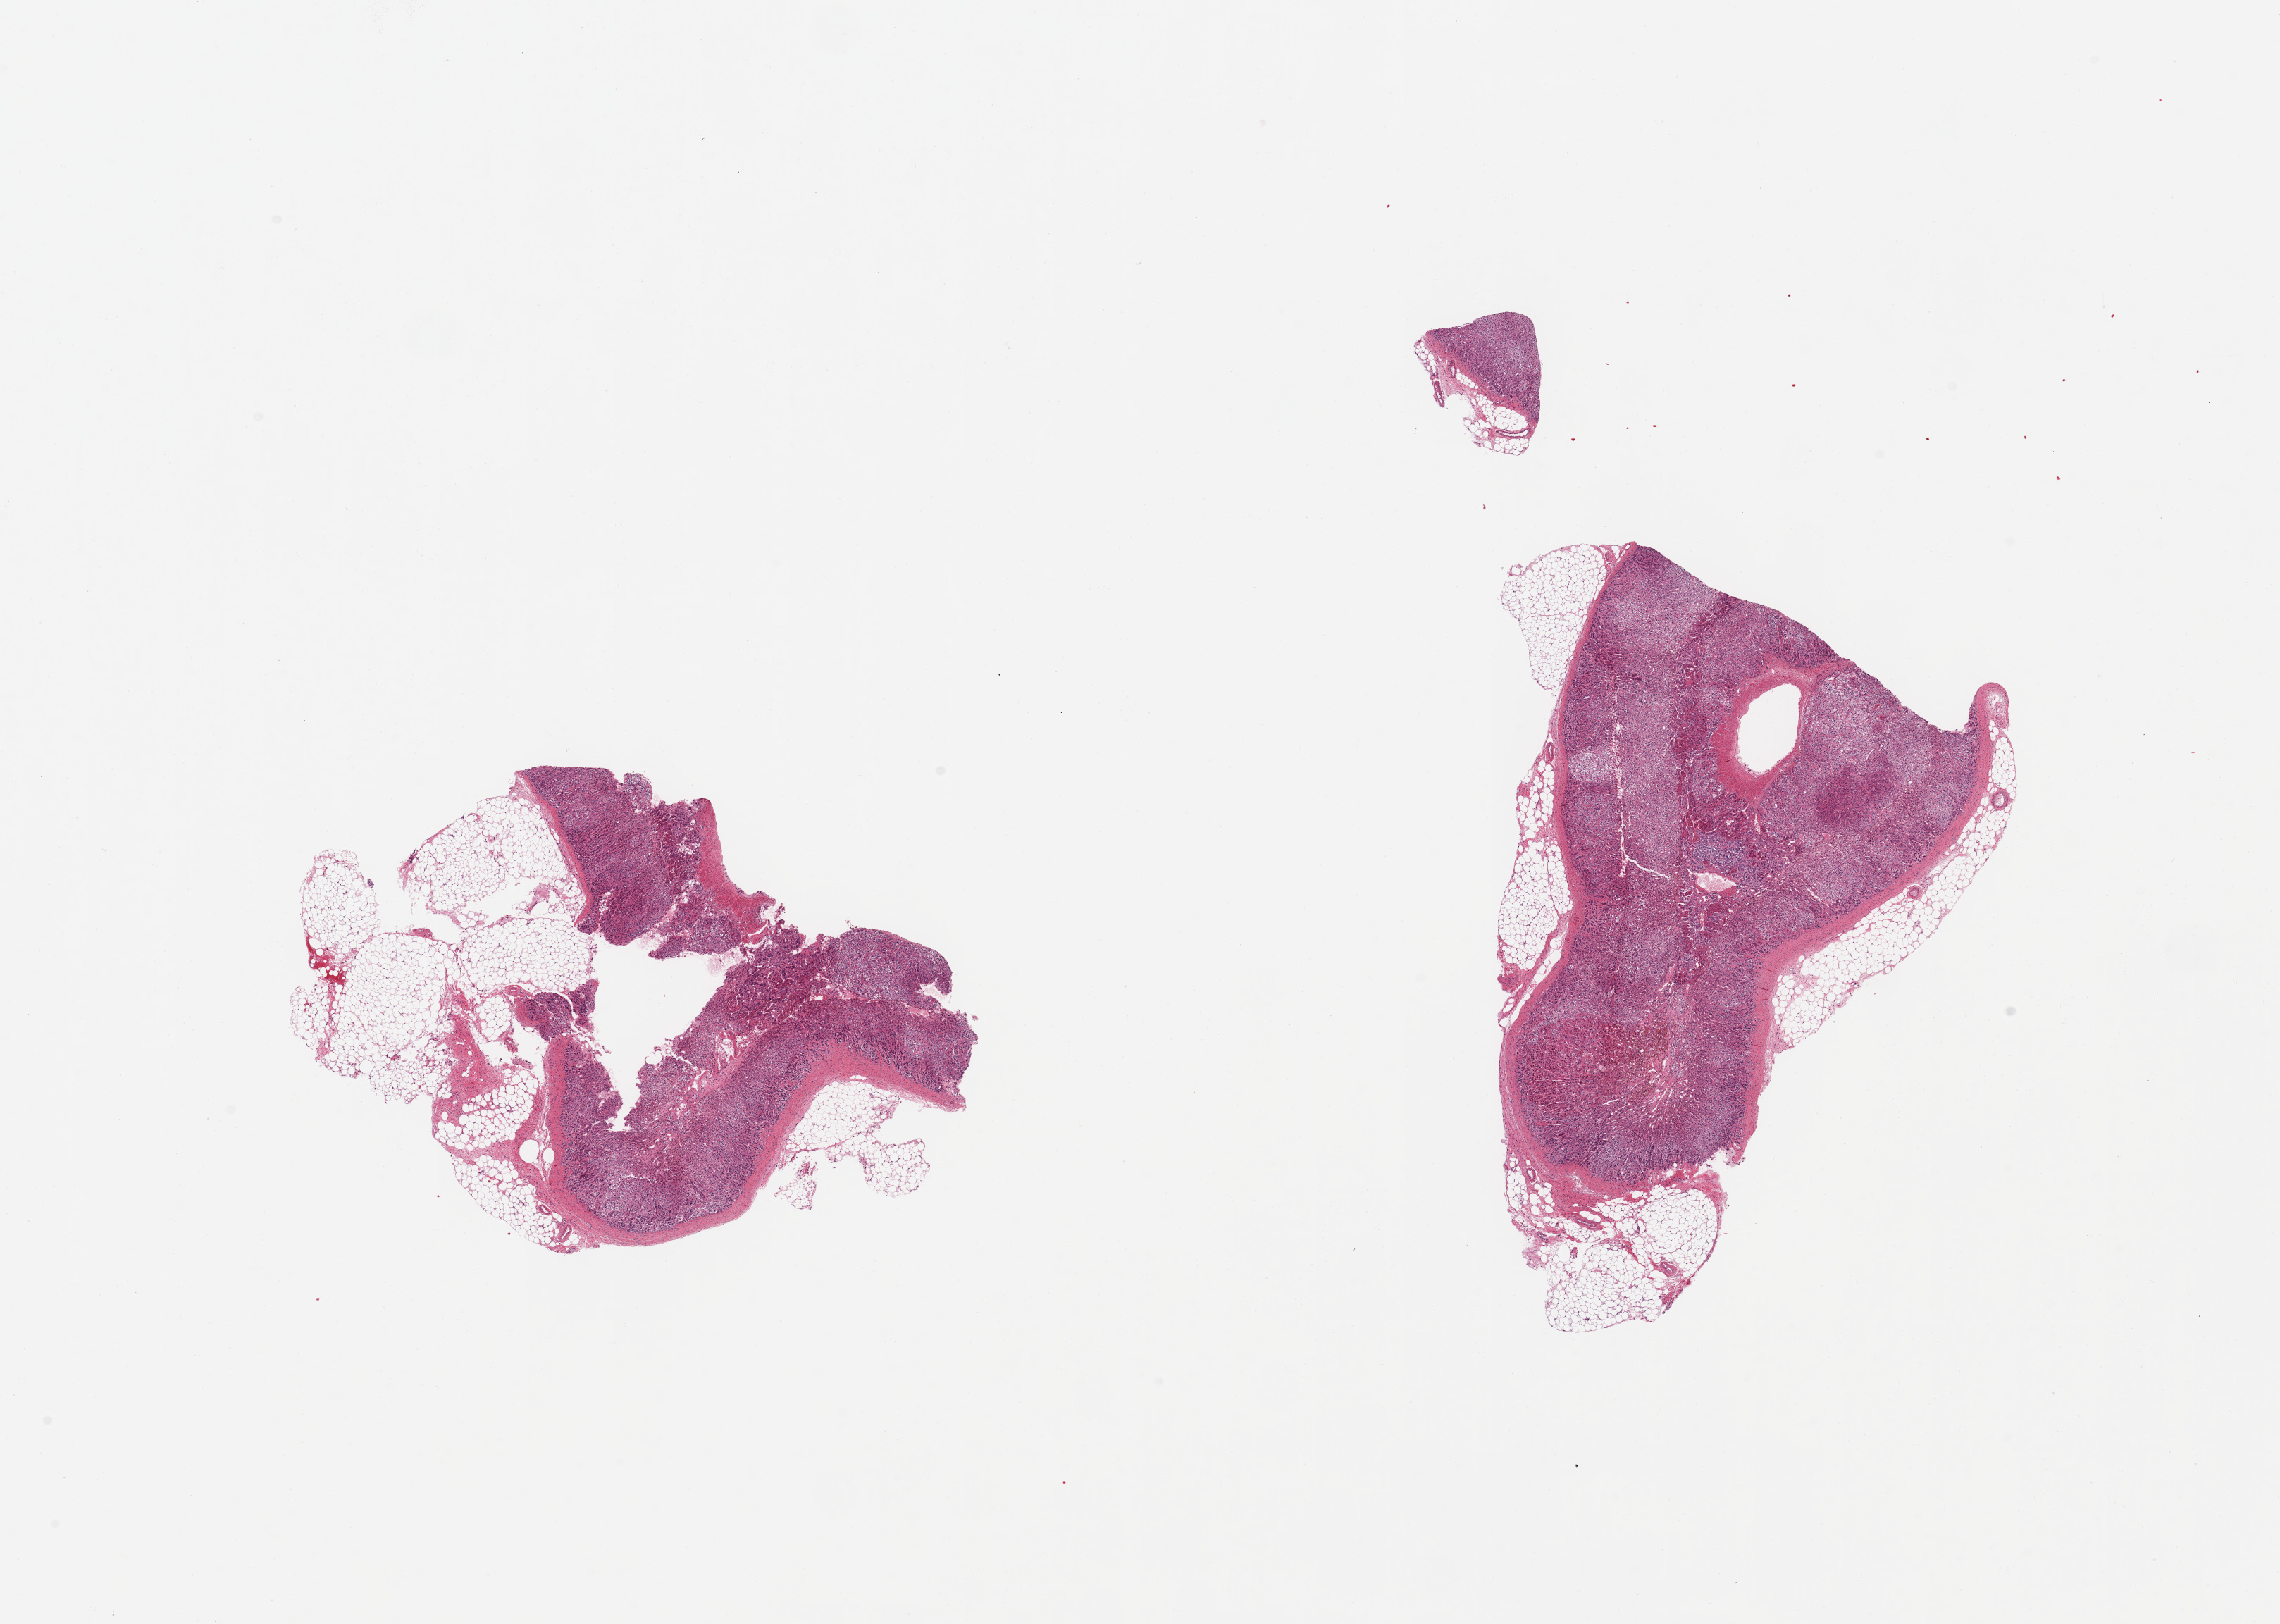
Digitized H&E-stained section — a low-resolution overview of the entire scanned area, about 25.6 x 18.2 mm (acquisition: 20x scan); PAXgene-fixed paraffin-embedded (PFPE) section; target tissue: adrenal gland; tissue donor sample. Donor: male.
Reviewer comment on this tissue sample: 2 pieces; include 20 and 40% attached fat, adrenal cortex and medulla.